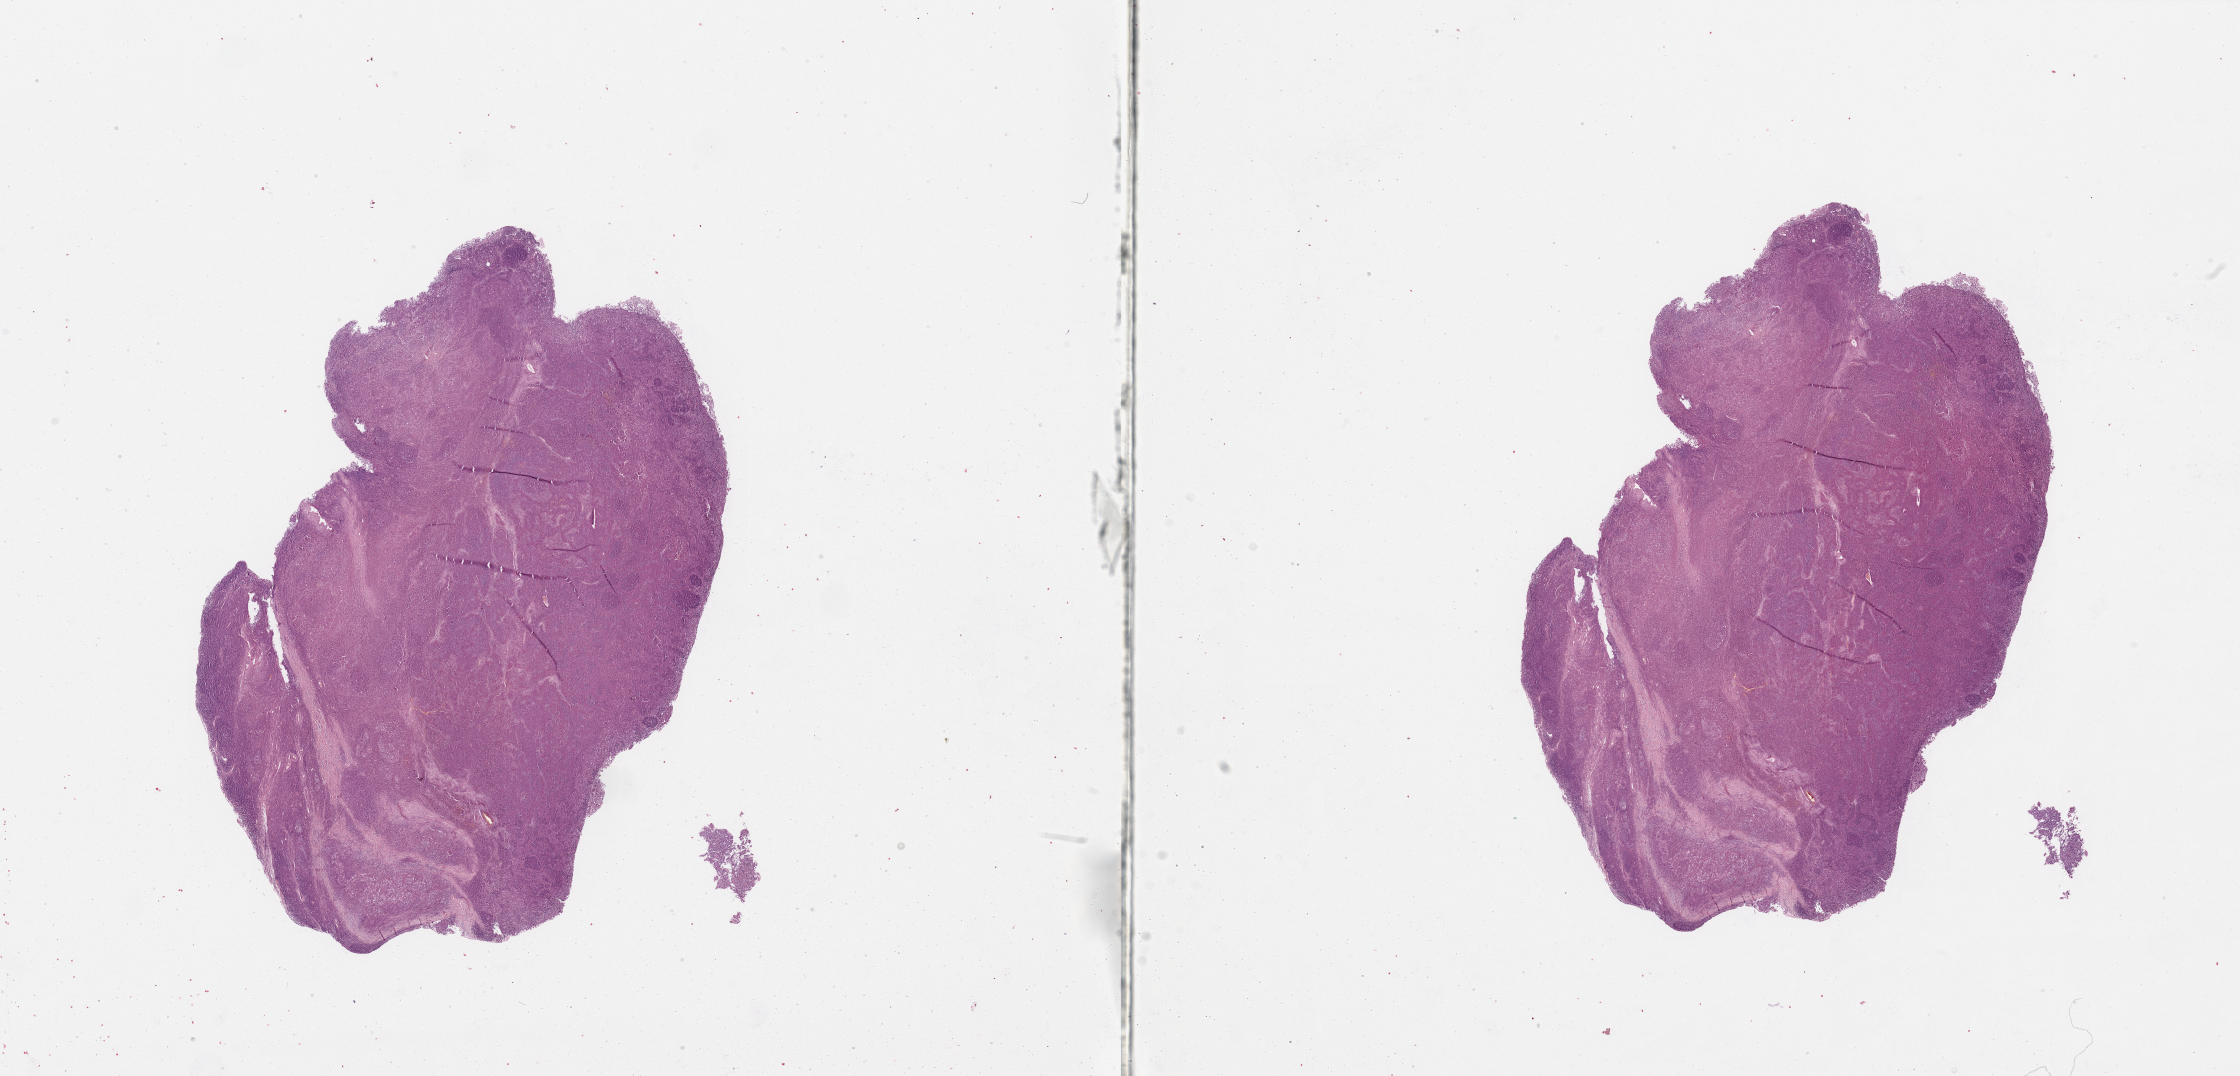
Whole-slide histology image, Hematoxylin and eosin (H&E) stained, low-resolution overview of the scanned area, about 35.4 x 17.0 mm (from a 20x scan). Melanoma tumour tissue; sampled site not recorded. Patient: female, age 53 years.
Histologic diagnosis: Malignant melanoma, NOS.